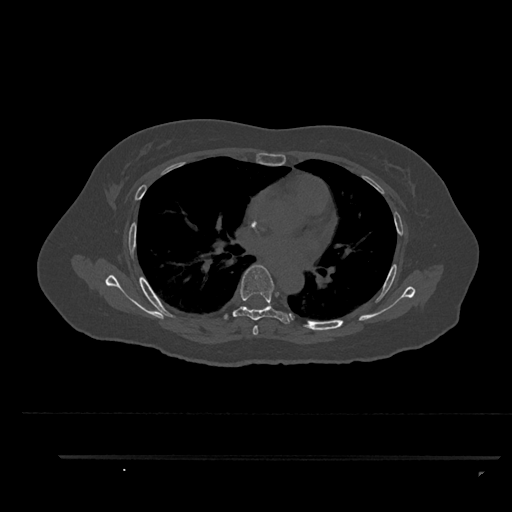
CT including the spine, one axial slice; slice 561 of 797 in the series (ordered by position); 120 kVp; bone window (W 1800 / L 400 HU); 0.5 mm slice thickness; 512 × 512 image matrix, field of view 408 × 408 mm. Female patient, age 44 years. From the clinical record (not read from this slice): primary cancer: renal; vertebrae with lytic lesions (as recorded): L1.
Annotated regions visible in this slice (semi-automatic segmentation, software-assisted and operator-edited):
- T5 vertebra: bounding box <253,325,258,335> (left, top, right, bottom; pixels)
- T6 vertebra: <223,265,292,335>